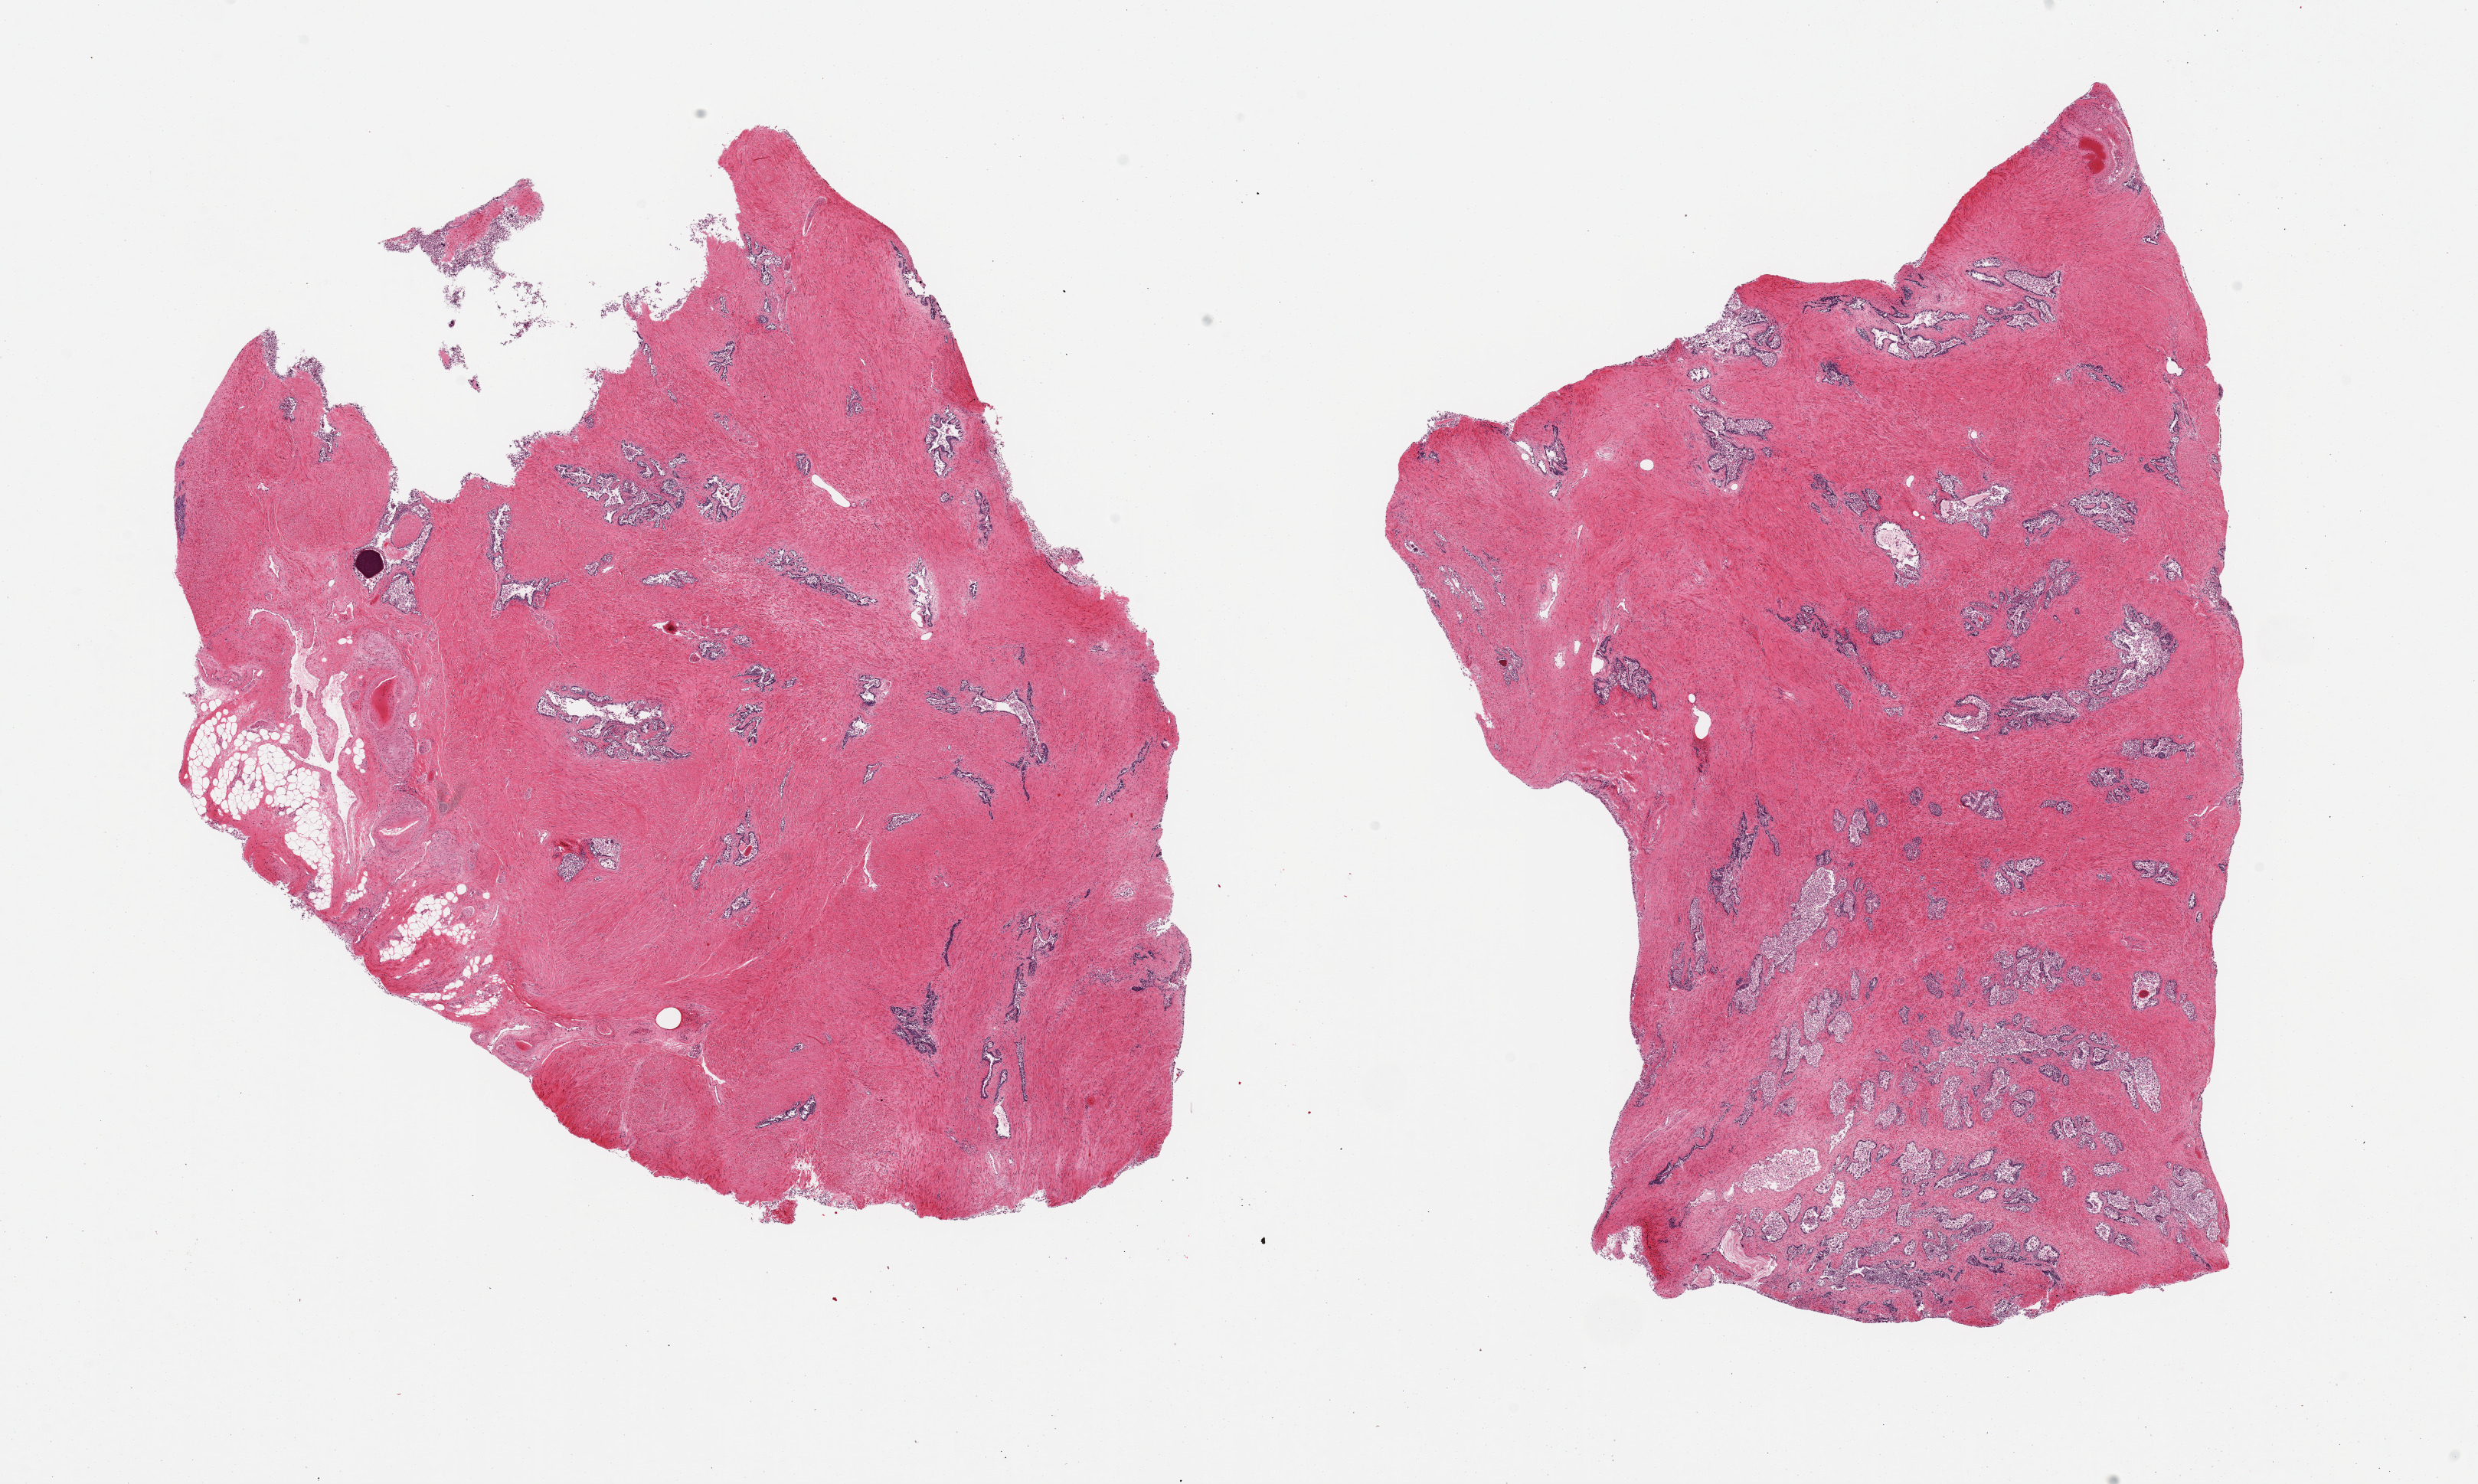
Whole-slide image, H&E stain, a low-resolution overview of the entire scanned area, about 25.6 x 15.3 mm (from a 20x scan); PAXgene-fixed, paraffin-embedded tissue; target tissue: prostate; donor tissue sample. Donor sex: male.
Review note (as recorded): 2 pieces; glands autolyzed, stroma intact.